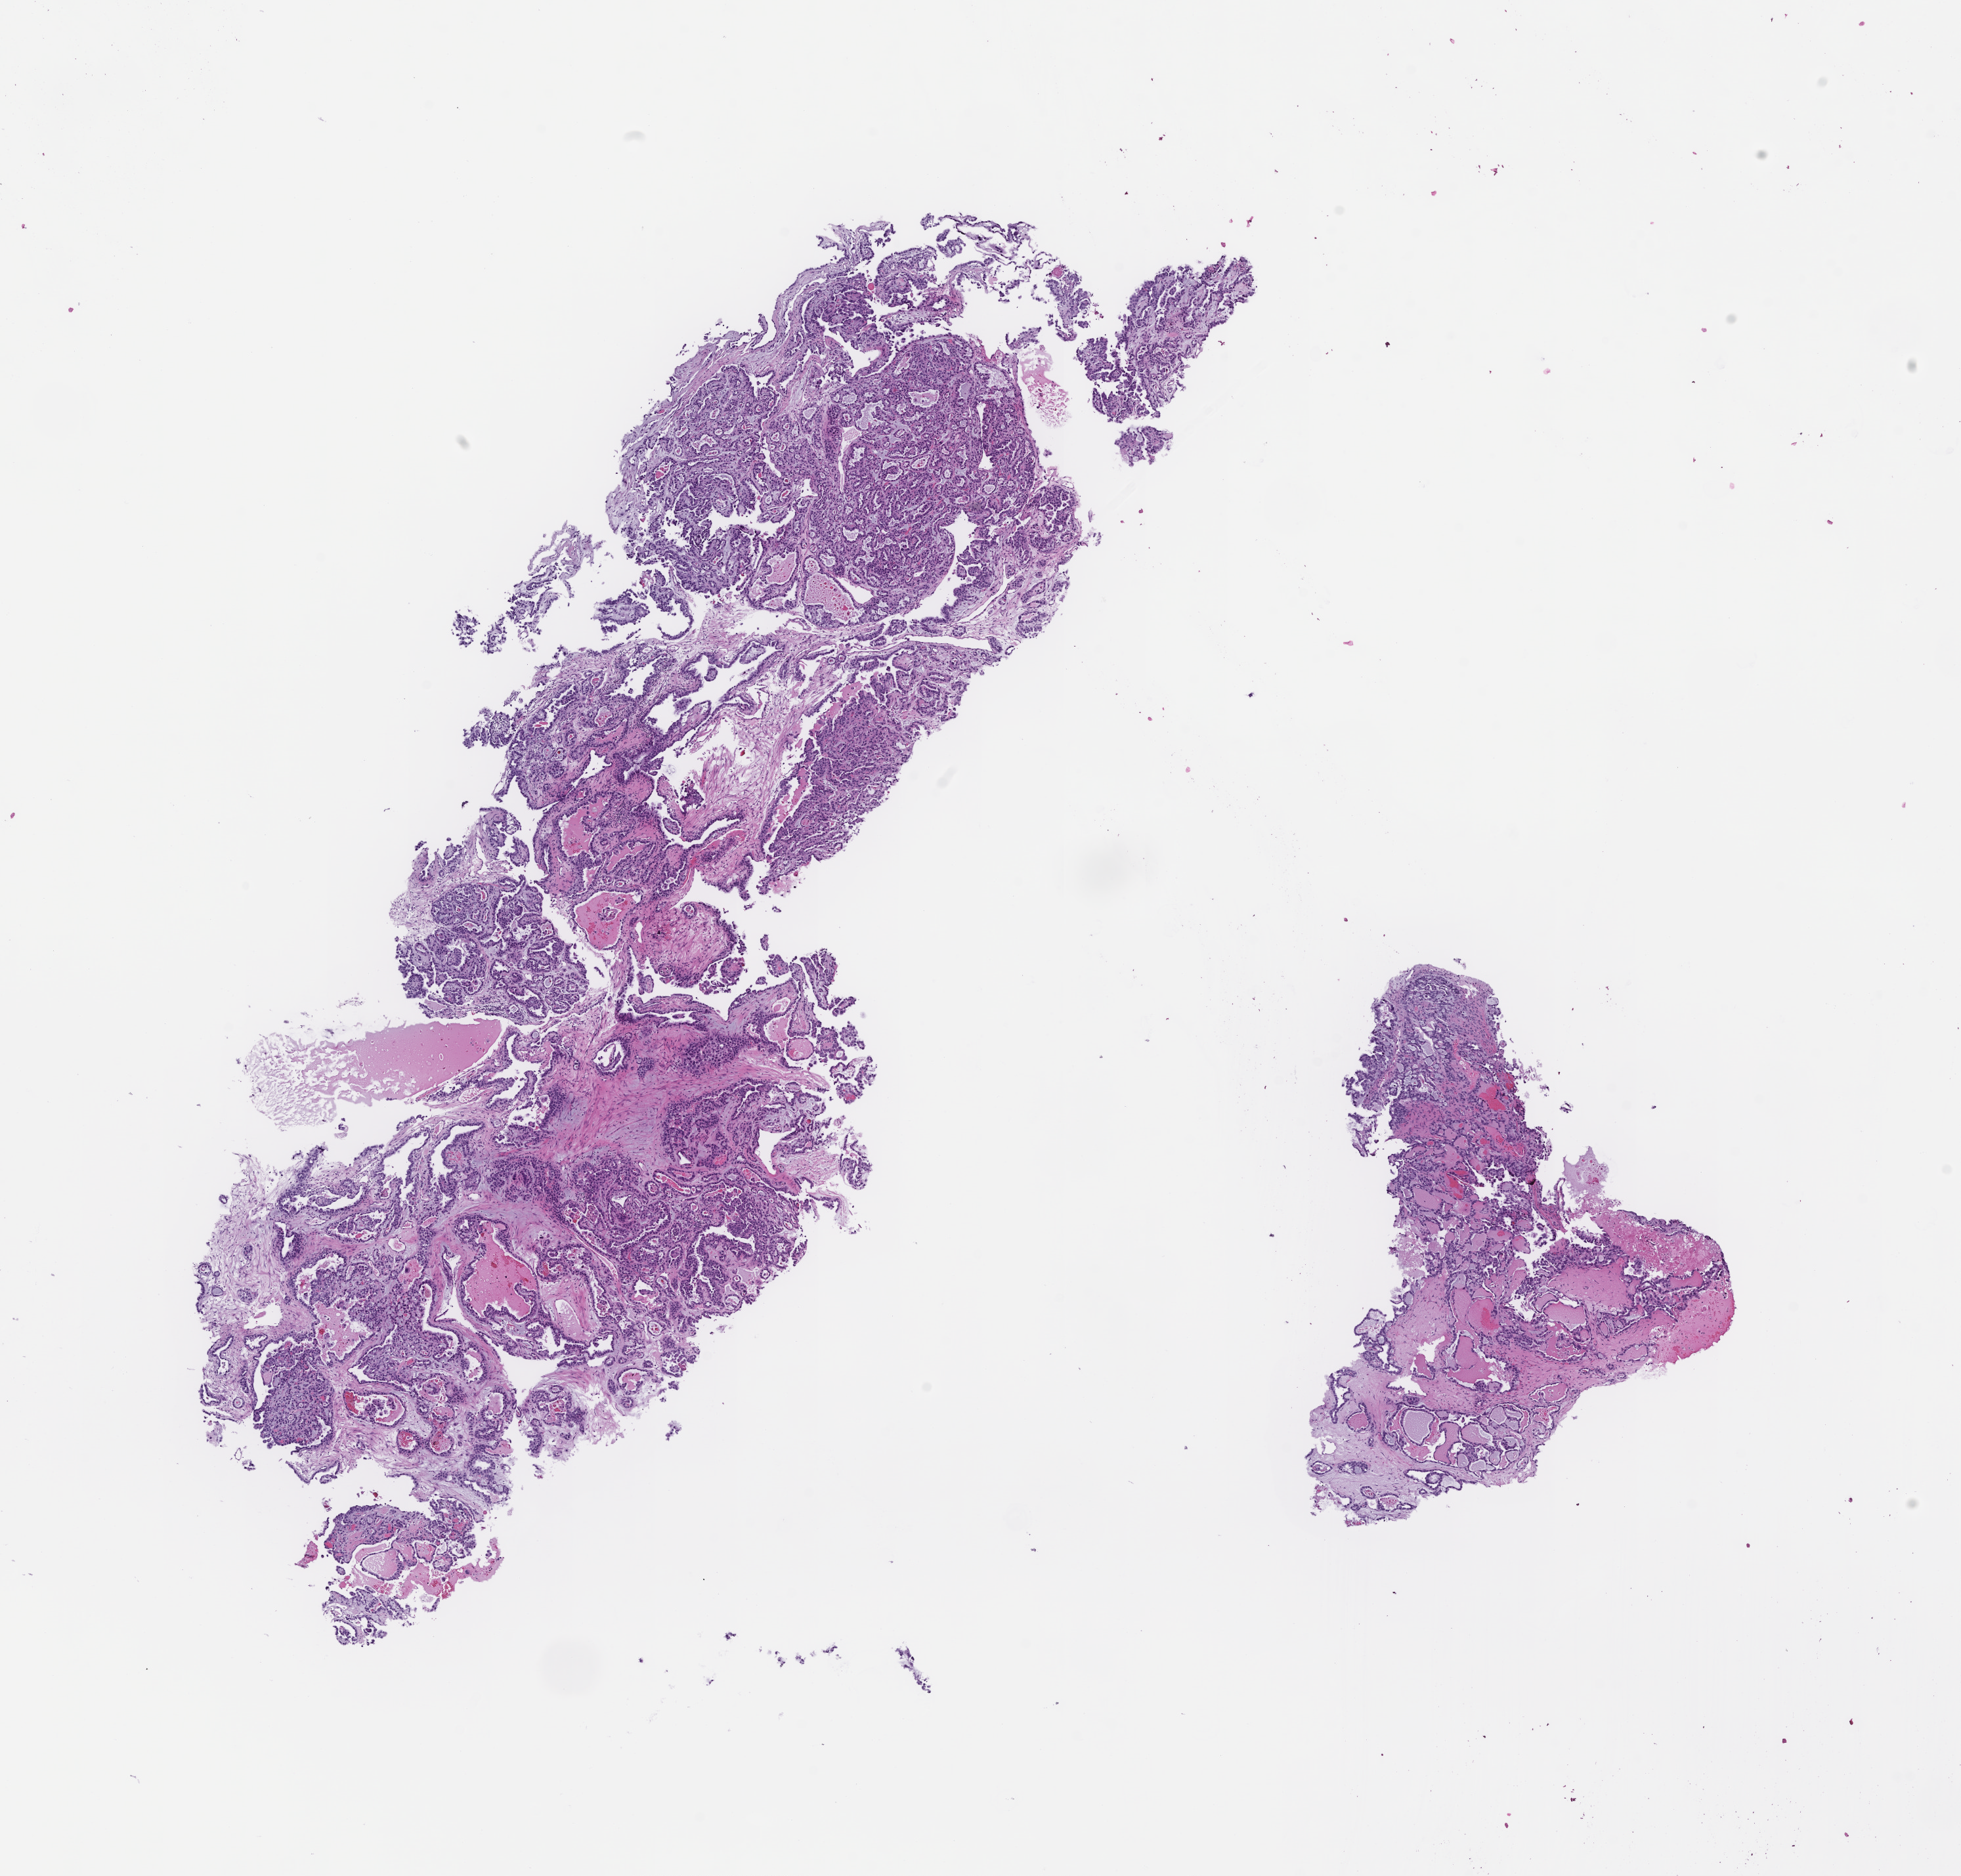
Digitized hematoxylin and eosin (H&E)-stained section, whole scanned area (about 12.1 x 11.5 mm) shown as a low-resolution overview. Formalin-fixed, paraffin-embedded (FFPE) tissue. Tissue site: ovary. Patient: female.
• this section: primary tumor
• diagnosis: Ovarian Carcinoma